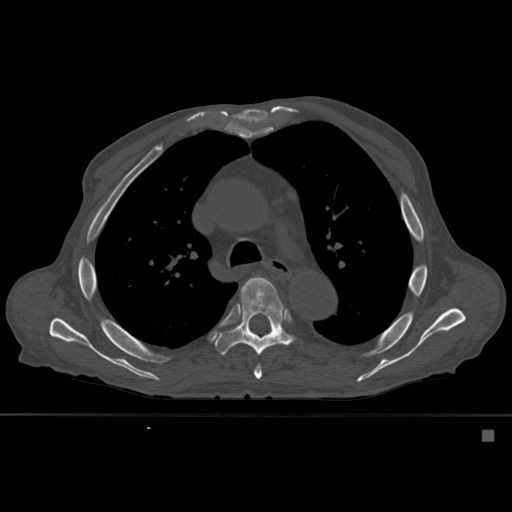
CT including the spine, one axial slice. Slice 388 of 527 in the series (ordered by position). Bone window (W 1800 / L 400 HU). 1.5 mm slice thickness. 512 × 512 image matrix, field of view 373 × 373 mm. Male patient, age 78 years. Case-level facts recorded for this patient, not image findings: primary cancer: prostate.
Annotated regions visible in this slice (semi-automatically segmented with operator editing):
- T5 vertebra: box from (x=250, y=346) to (x=262, y=380) px
- T6 vertebra: (x=215, y=277)–(x=294, y=356)